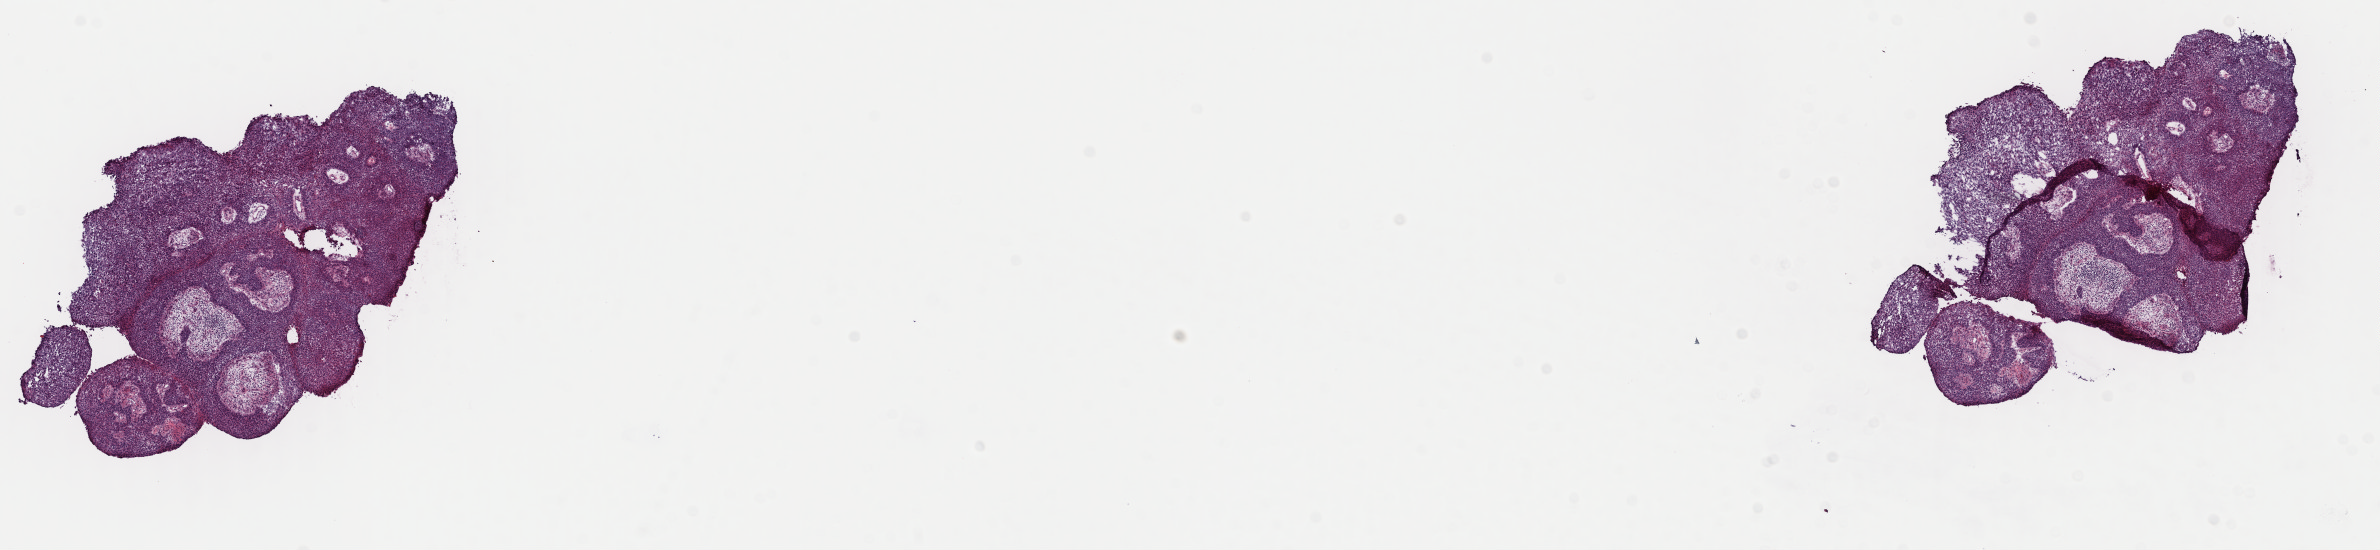
Whole-slide histology image, H&E — whole scanned area (about 18.8 x 4.3 mm, from a 40x scan) shown as a low-resolution overview, frozen section, cervix, primary tumour sample. Patient: female, age at initial diagnosis 43 years. Histologic grade: G3 (poorly differentiated). Composition of this section per pathologist review: tumour cells 90%, tumour nuclei 90%, normal cells 0%, stromal cells 5%, necrosis 5%. Inflammatory infiltration, as recorded: lymphocyte infiltration 40%, monocyte infiltration 20%, neutrophil infiltration 20%.
* diagnosis: Papillary squamous cell carcinoma (cervix uteri)
* FIGO stage: IB2